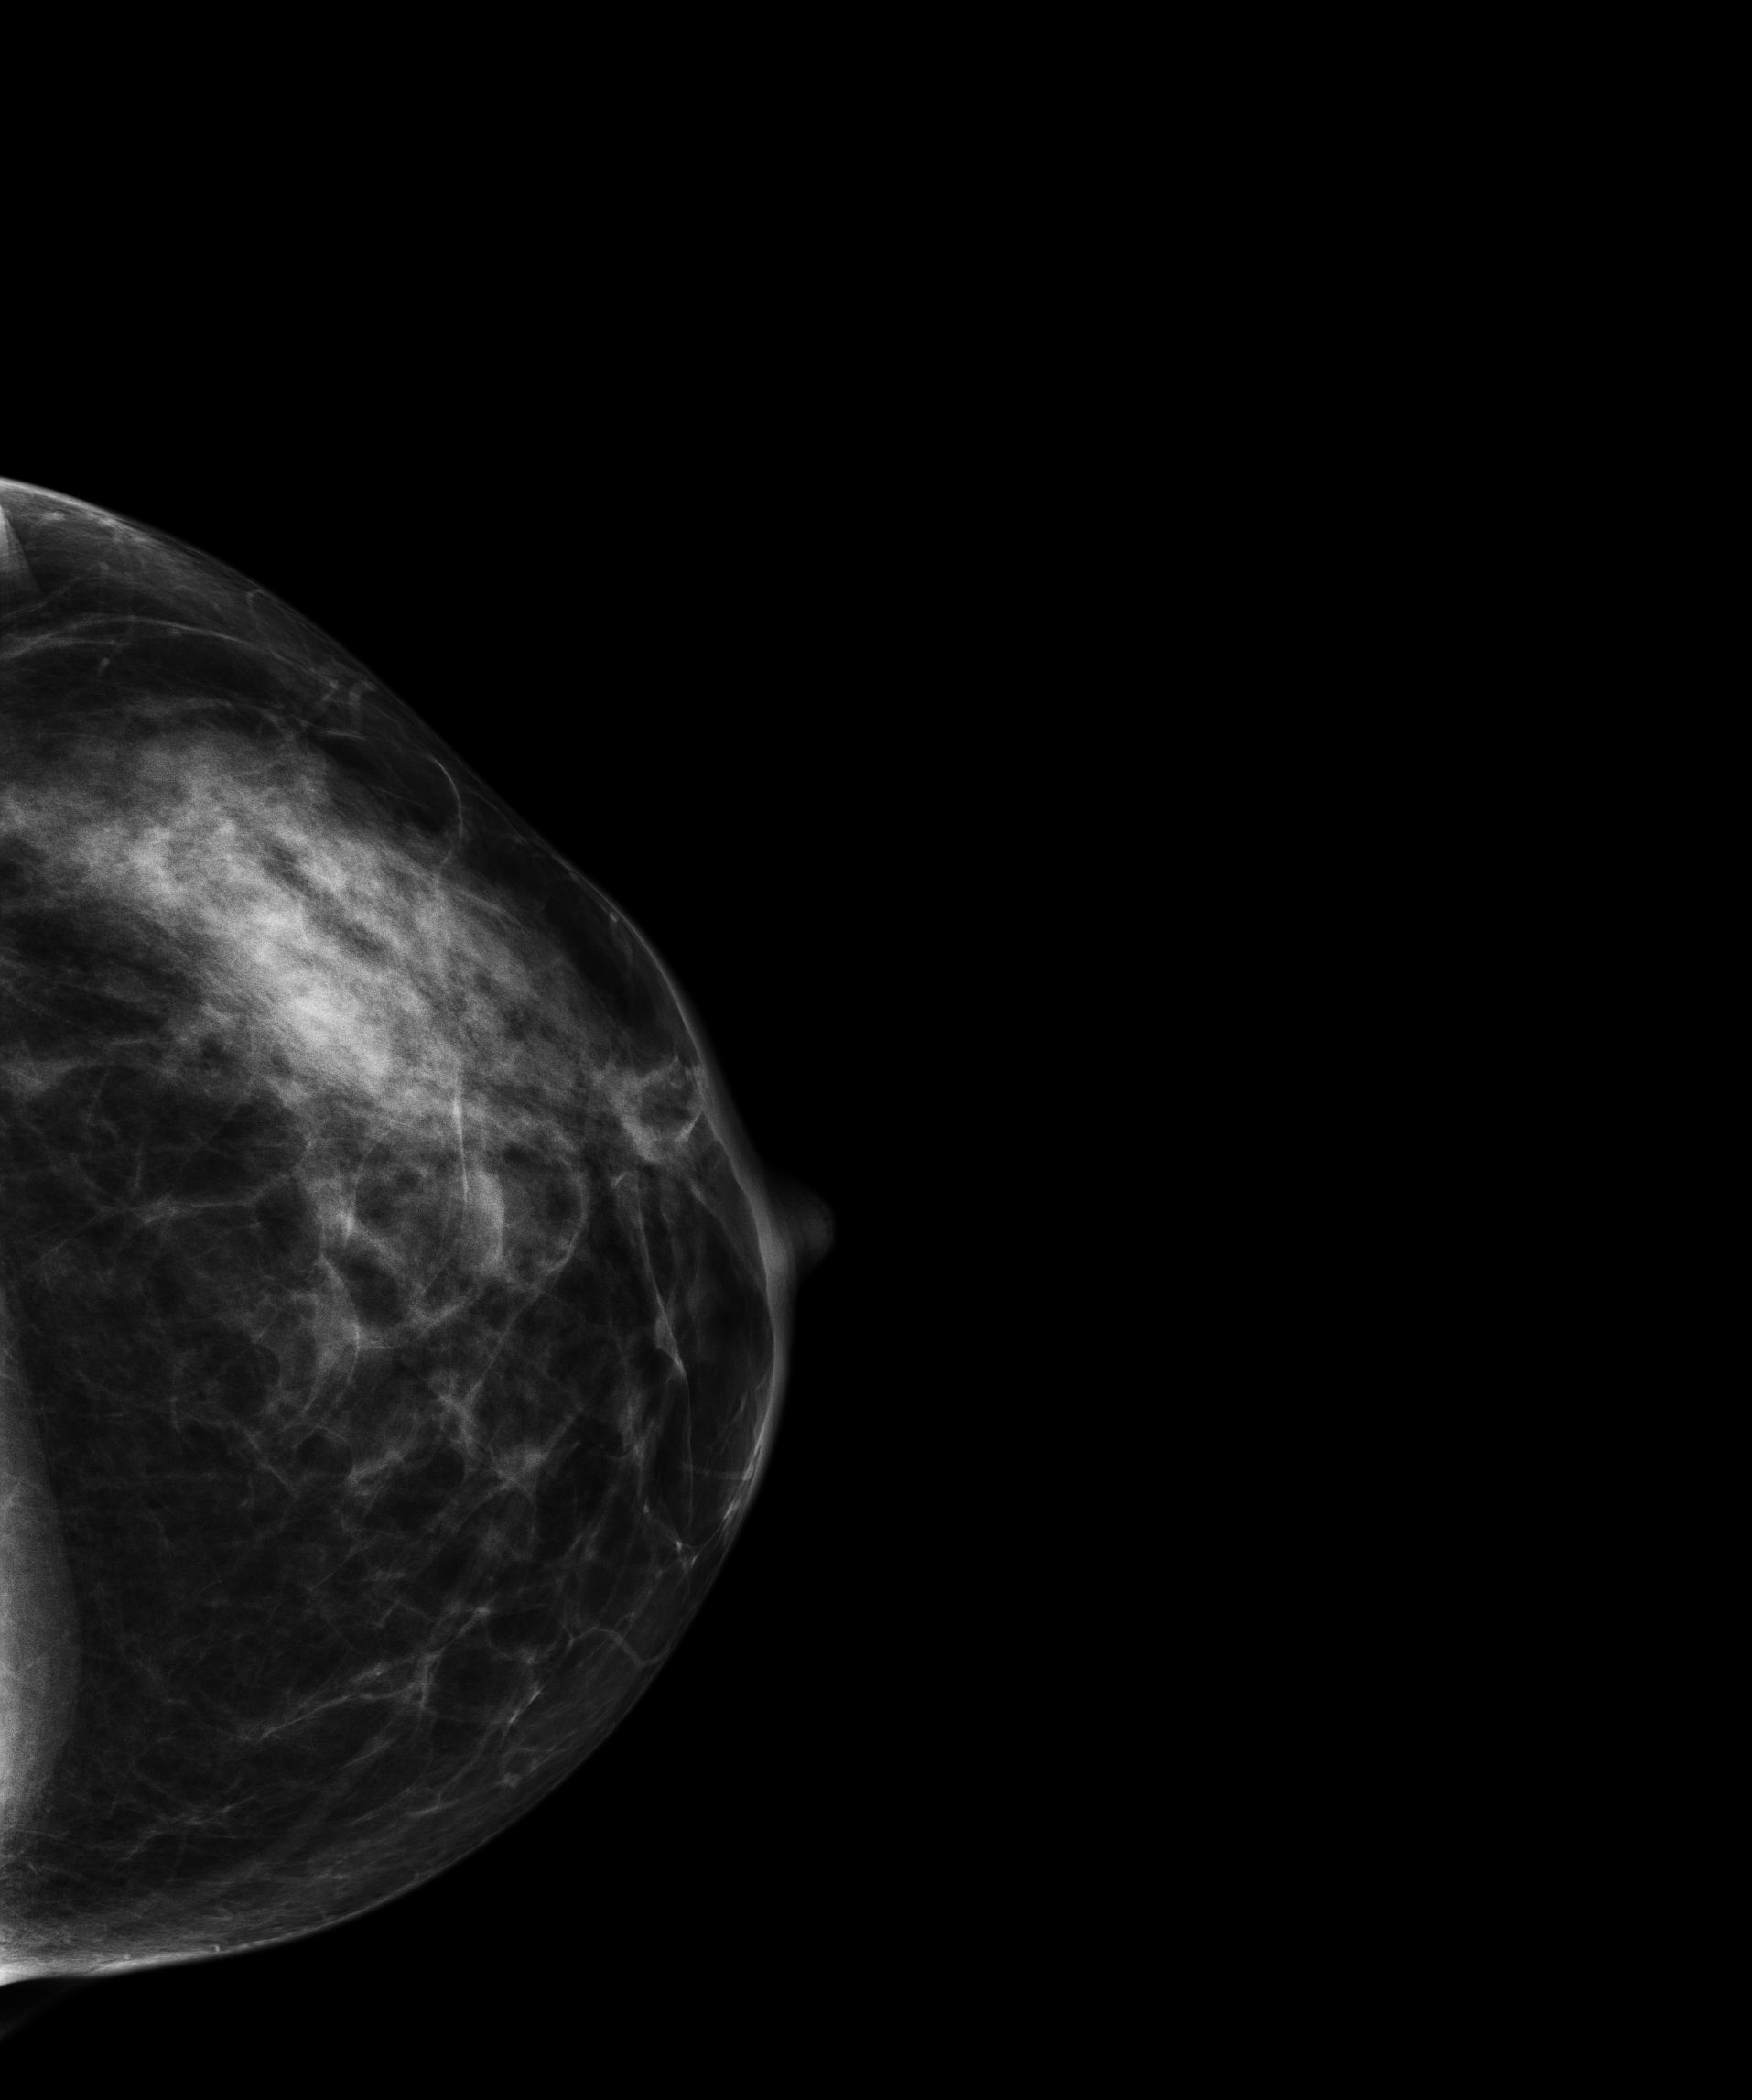
Full-field digital mammogram (FFDM), left breast, cranio-caudal projection, screening examination, compressed breast thickness 57 mm. Patient: female, 45 years.
Breast density at the screening exam (both breasts): heterogeneously dense (BI-RADS density category c). Final BI-RADS assessment for this screening round (tomosynthesis exam, both breasts): category 1. Recall: no recall after this screen.